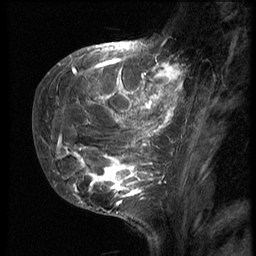
Breast MRI (dynamic contrast-enhanced), one sagittal slice; slice 17 of 62 in the series (ordered by position); 3 images stored at this slice position (order not interpretable as contrast timing); 1.5 T; TE 4.2 ms, TR 9 ms; 2.5 mm slice thickness; 256 × 256 image matrix. Female patient, age 28 years. Case-level facts recorded for this patient, not image findings: setting: breast cancer imaged before/during neoadjuvant chemotherapy.
Annotated regions visible in this slice (semi-automatic segmentation, software-assisted and operator-edited):
- analysis volume of interest (the breast-tissue region the enhancement analysis was run in; not a lesion): bounding box (x1, y1, x2, y2) in pixels: (42, 51, 192, 207)
- tumour enhancement mask (voxels above the 140 % enhancement threshold inside the analysis volume of interest): (55, 58, 184, 205)